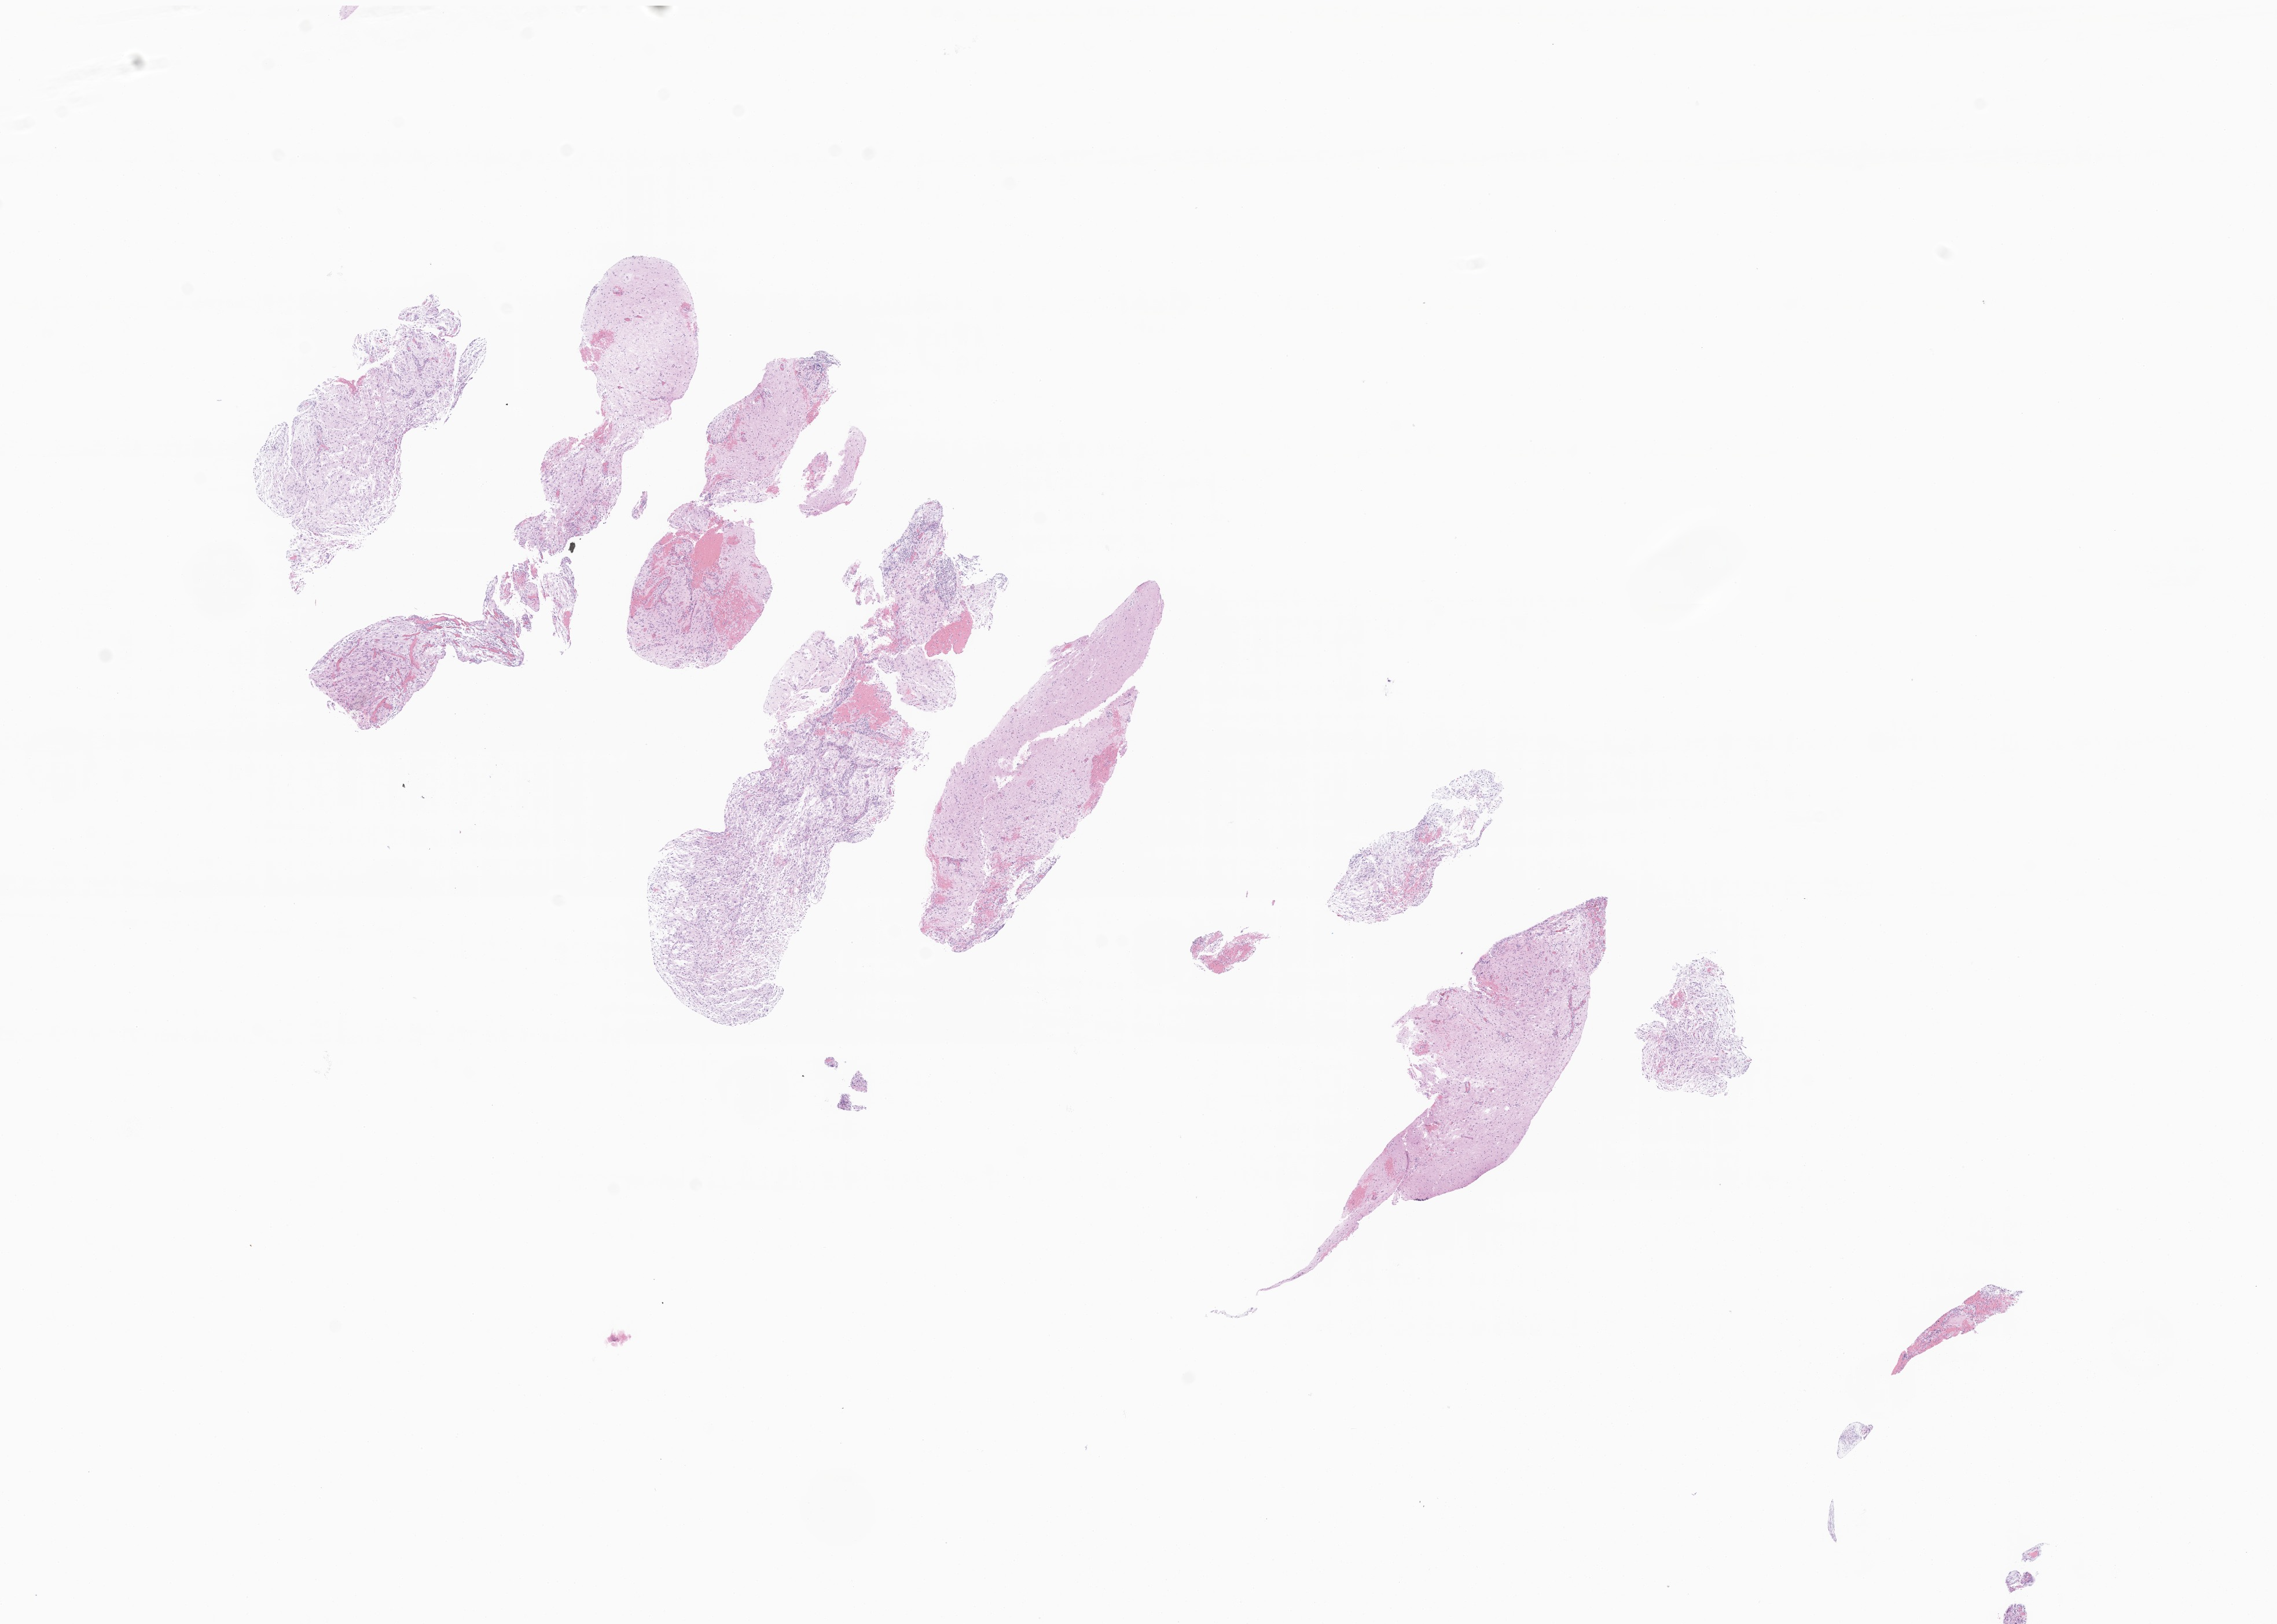
Haematoxylin and eosin whole-slide image of tumor tissue from the frontal lobe, a low-resolution overview of the entire scanned area, about 16.6 x 11.8 mm. Formalin-fixed paraffin-embedded section. Patient: male, age 200 months (16 years 8 months).
• diagnosis: Glioma, malignant